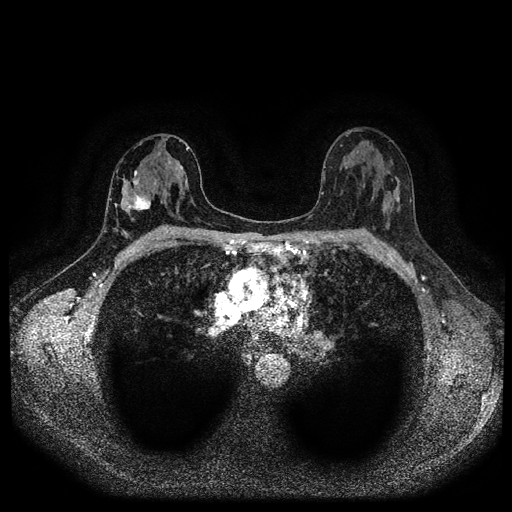
Breast MRI (dynamic contrast-enhanced, multi-phase), one axial slice. Slice 58 of 116 in the series (ordered by position). Dynamic contrast-enhanced series, time point 2 of 5 at this slice position (early post-contrast). 1.5 T. TE 2.7 ms, TR 5.4 ms. 2 mm slice thickness. 512 × 512 image matrix, field of view 330 × 330 mm. Patient: female, 42 years.
Outlined on this slice (semi-automatically segmented with operator editing):
- breast lesion (labelled 'tumour' in the annotation; benign lesions carry a separate 'benign' label): bounding box <126,177,151,213> (left, top, right, bottom; pixels)